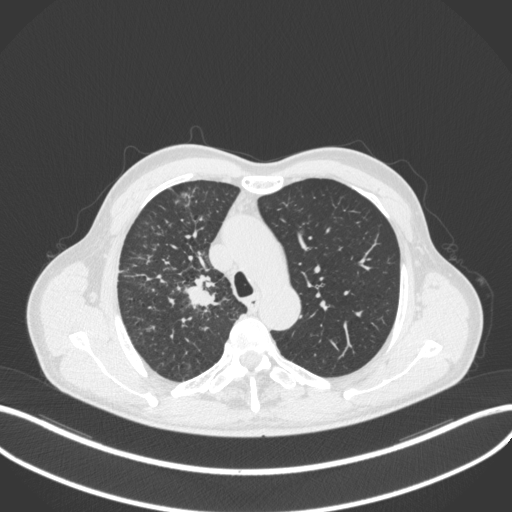
Chest CT, one axial slice; slice 355 of 490 in the series (ordered by position); reconstruction kernel B31f; 120 kVp; lung window (W 1500 / L -600 HU); 1 mm slice thickness; 512 × 512 image matrix. Patient: male, 69 years. Case-level facts recorded for this patient, not image findings: clinical TNM (as recorded): T2a N0 M0.
Structures marked on this image (bounding box drawn by a radiologist):
- lung tumour (recorded histology: adenocarcinoma): bounding box [x1, y1, x2, y2] px = [183, 271, 223, 313]